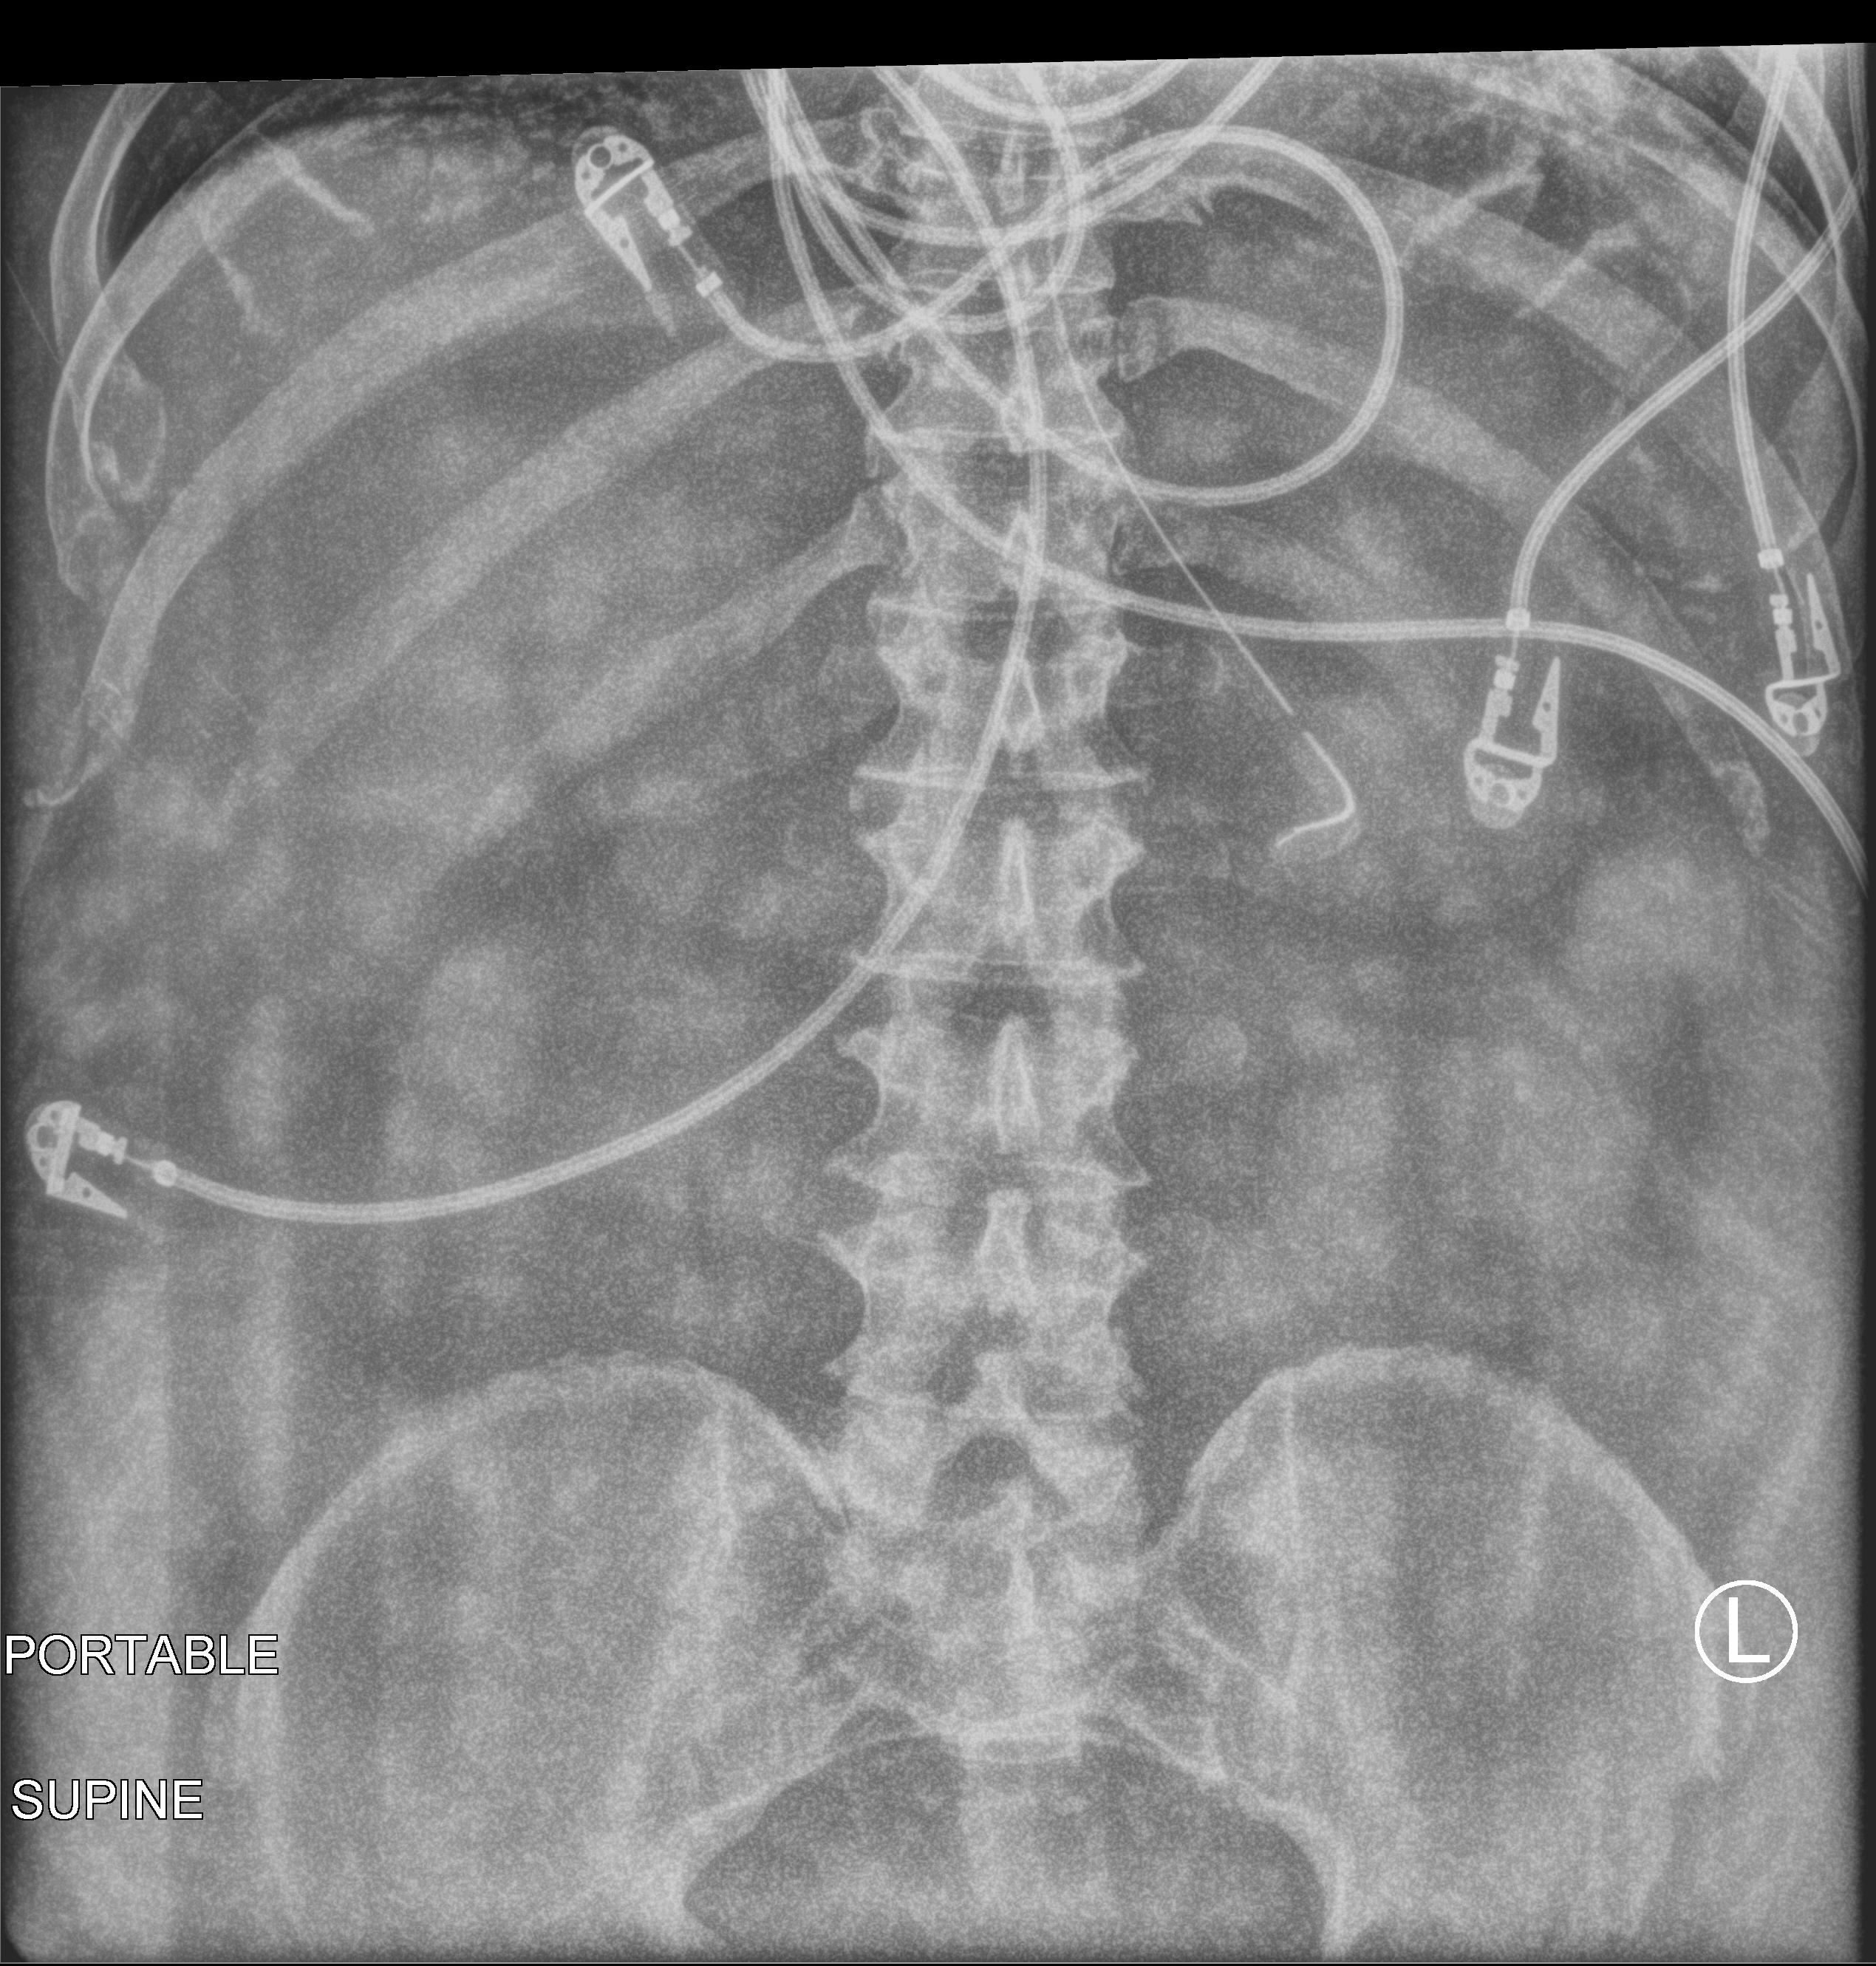
Abdomen X-ray (portable); anteroposterior (AP) projection. Patient hospitalised with COVID-19; male, aged 60–74 years.
From the hospital-stay record, not from the radiograph (when in the stay this image was taken is not recorded):
- admitted to intensive care during this hospital stay: yes
- diabetes (admission record): no
- mechanically ventilated during this hospital stay: yes